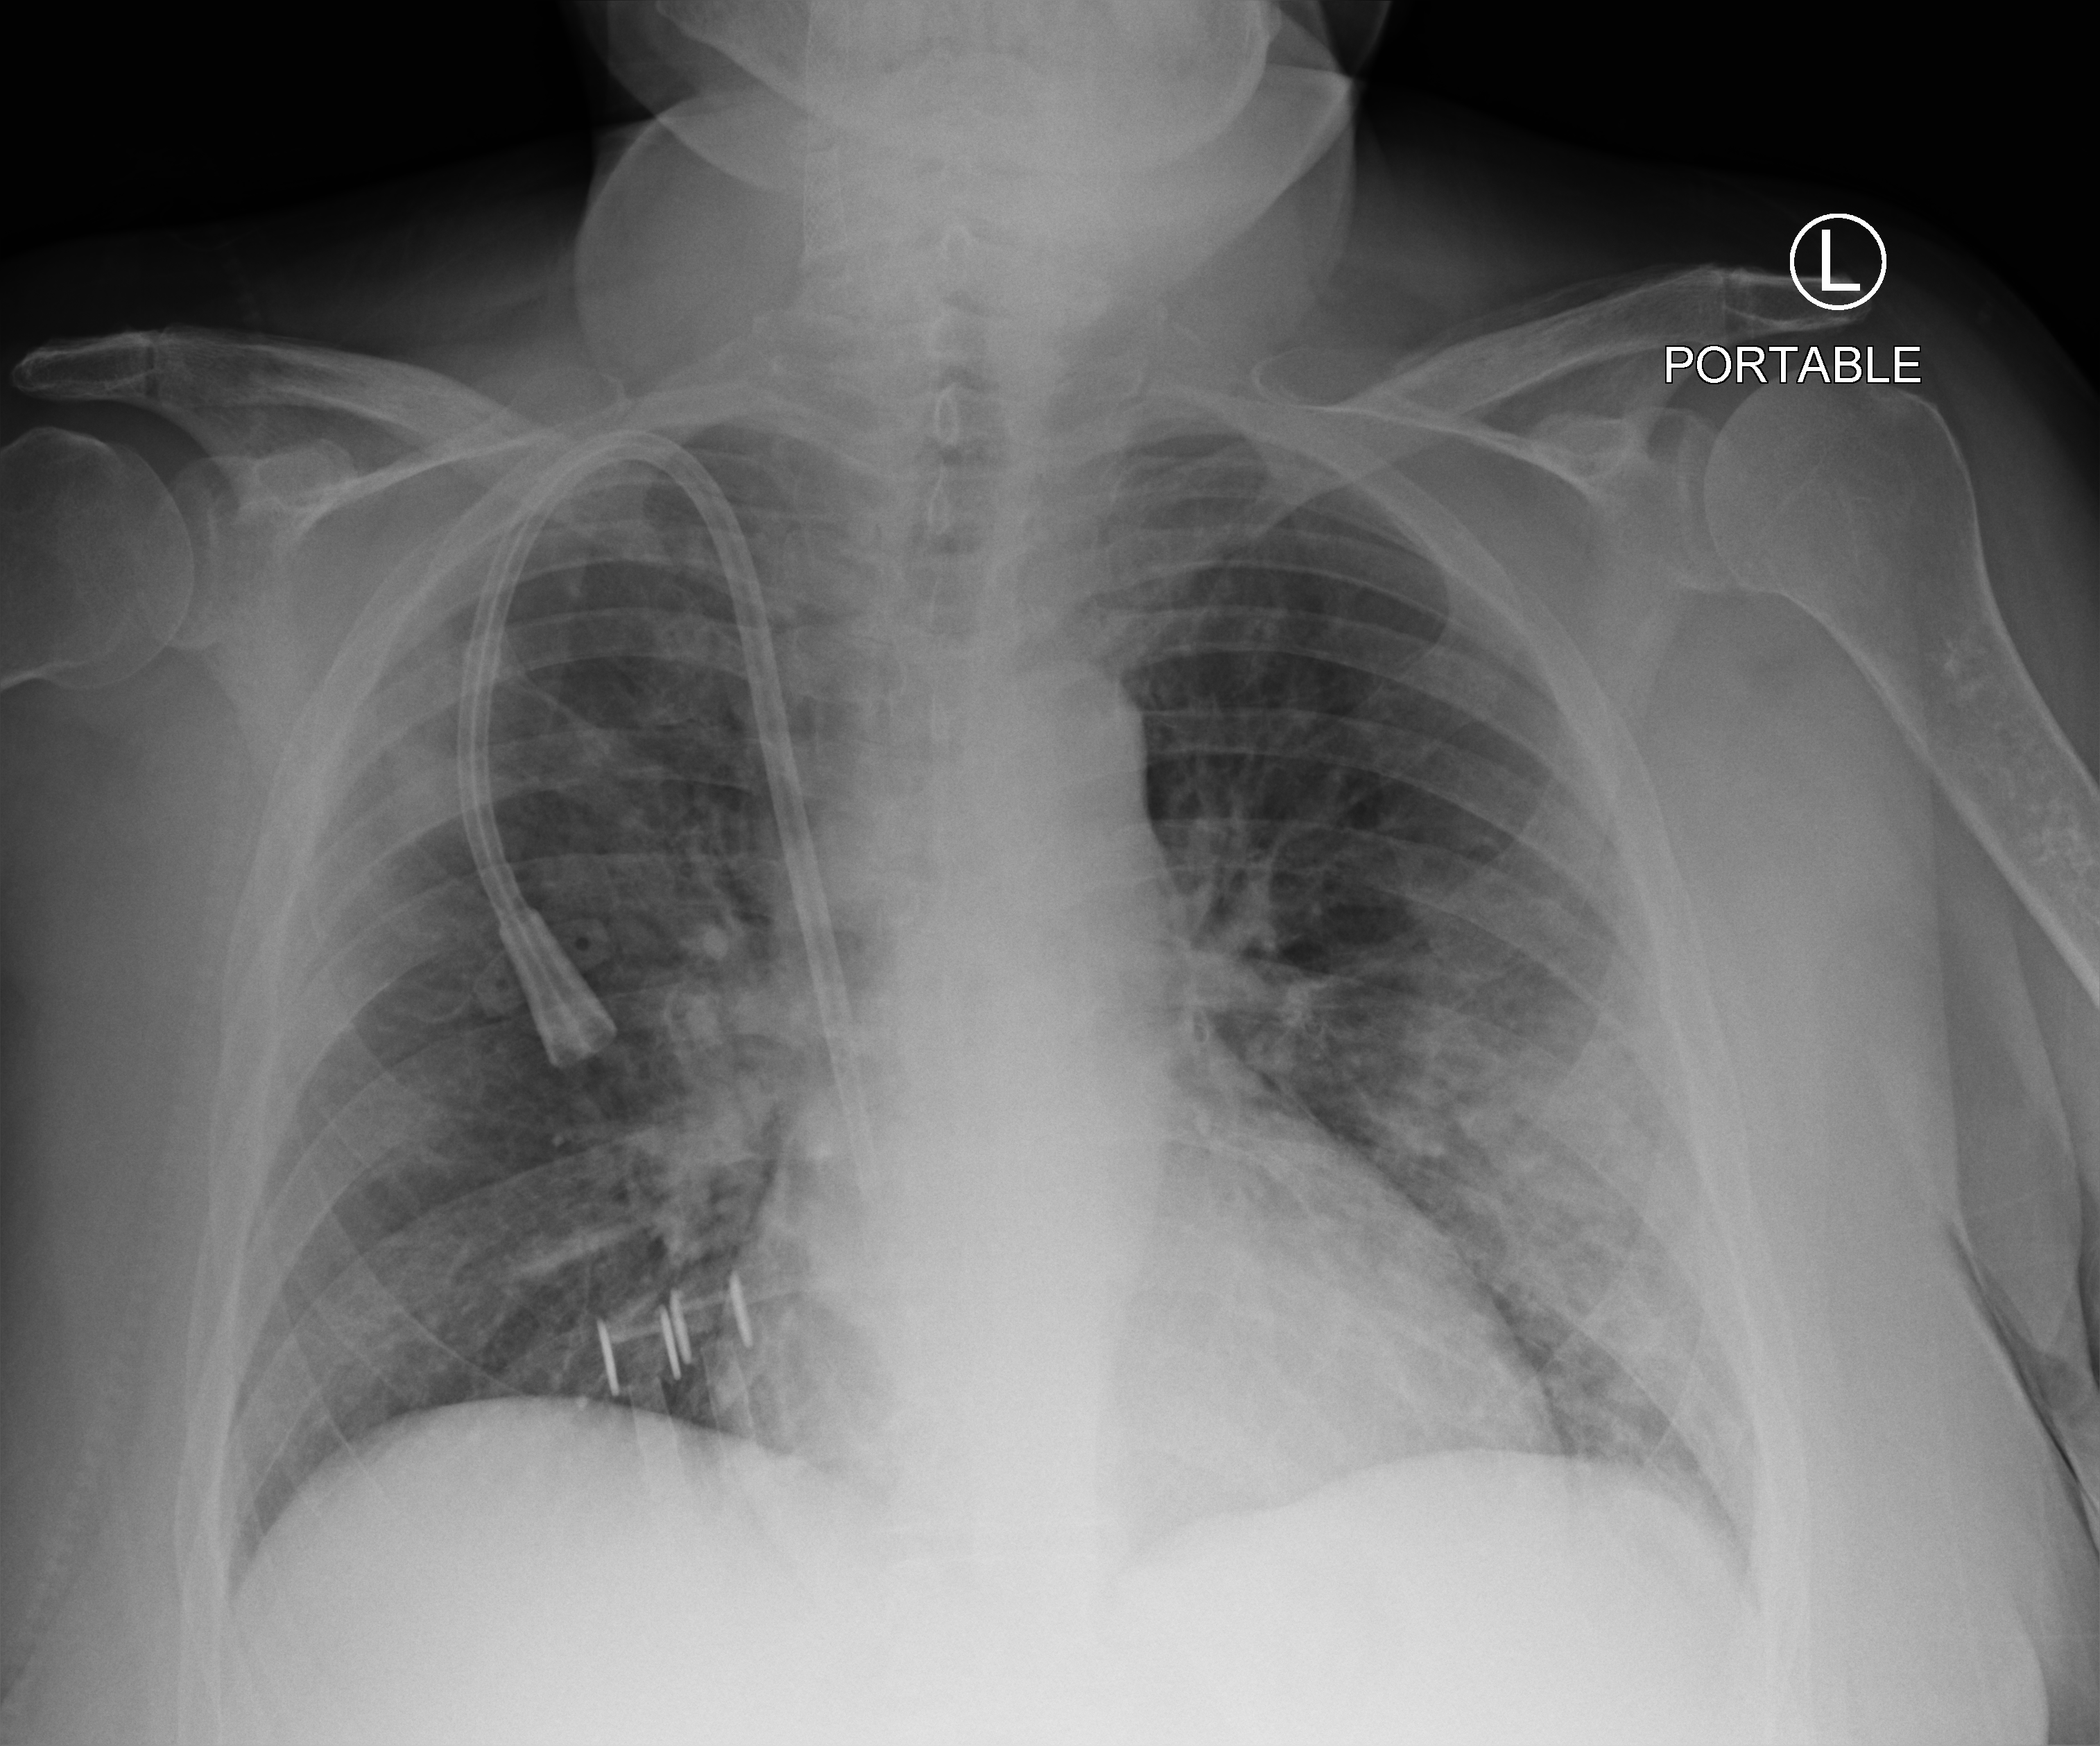
Bedside chest radiograph (computed radiography), anteroposterior (AP) projection. Female patient hospitalised with COVID-19, age 60–74 years.
Hospital-stay facts (about this admission, not read from this image; timing relative to this image not recorded):
- admitted to intensive care during this hospital stay: no